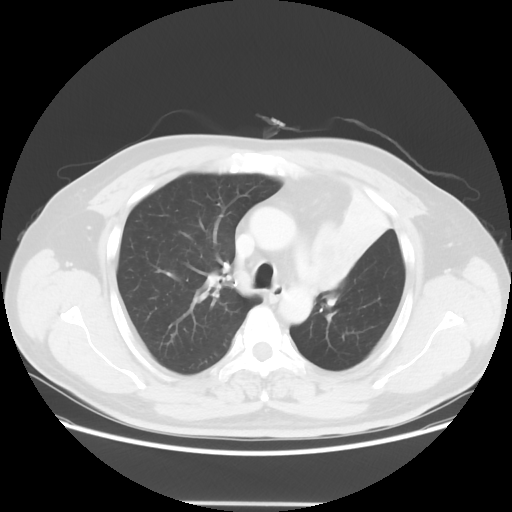
Chest CT, one axial slice; slice 42 of 62 in the series (ordered by position); lung window (W 1500 / L -600 HU); 5 mm slice thickness; 512 × 512 image matrix, field of view 403 × 403 mm. Patient: male, 49 years. Case-level facts recorded for this patient, not image findings: clinical TNM (as recorded): T3 N3 M1c.
Annotated regions visible in this slice (bounding box drawn by a radiologist):
- lung tumour (recorded histology: squamous cell carcinoma): bounding box <305,218,354,298> (left, top, right, bottom; pixels)